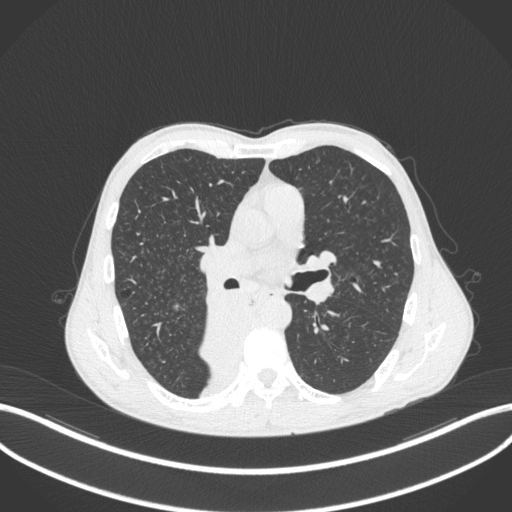
Chest CT, one axial slice; position 215 of 371 along the scan axis; lung window (W 1500 / L -600 HU); 1 mm slice thickness; 512 × 512 image matrix, field of view 400 × 400 mm. Patient: male, 58 years. Case-level facts recorded for this patient, not image findings: clinical TNM (as recorded): T3 N1 M1.
Structures marked on this image (bounding box drawn by a radiologist):
- lung tumour (recorded histology: squamous cell carcinoma): box from (x=194, y=286) to (x=255, y=375) px